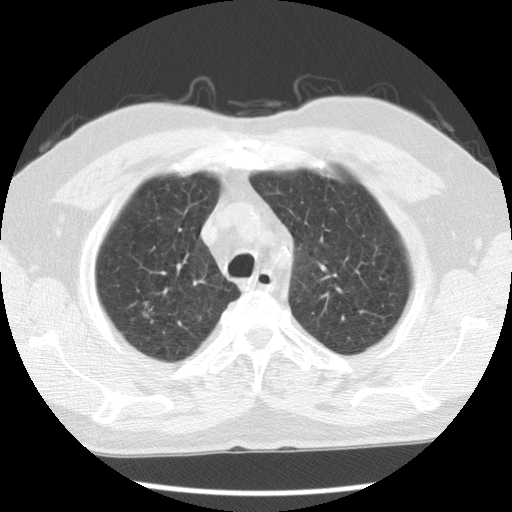
Low-dose screening chest CT, axial slice; baseline annual screen; lung window (W 1500 / L -600 HU); 2.5 mm slice thickness; standard (soft-tissue) reconstruction kernel (STANDARD). Male, age 68 years at enrolment. Former smoker at enrolment.
Lesion marked by an expert reader, bounding box <129,295,171,335> (left, top, right, bottom; pixels). Reader record for this screening exam (exam-level; its link to the box is not recorded): non-calcified nodule or mass ≥4 mm, right upper lobe, 9 × 7 mm, poorly defined margins, ground glass attenuation.